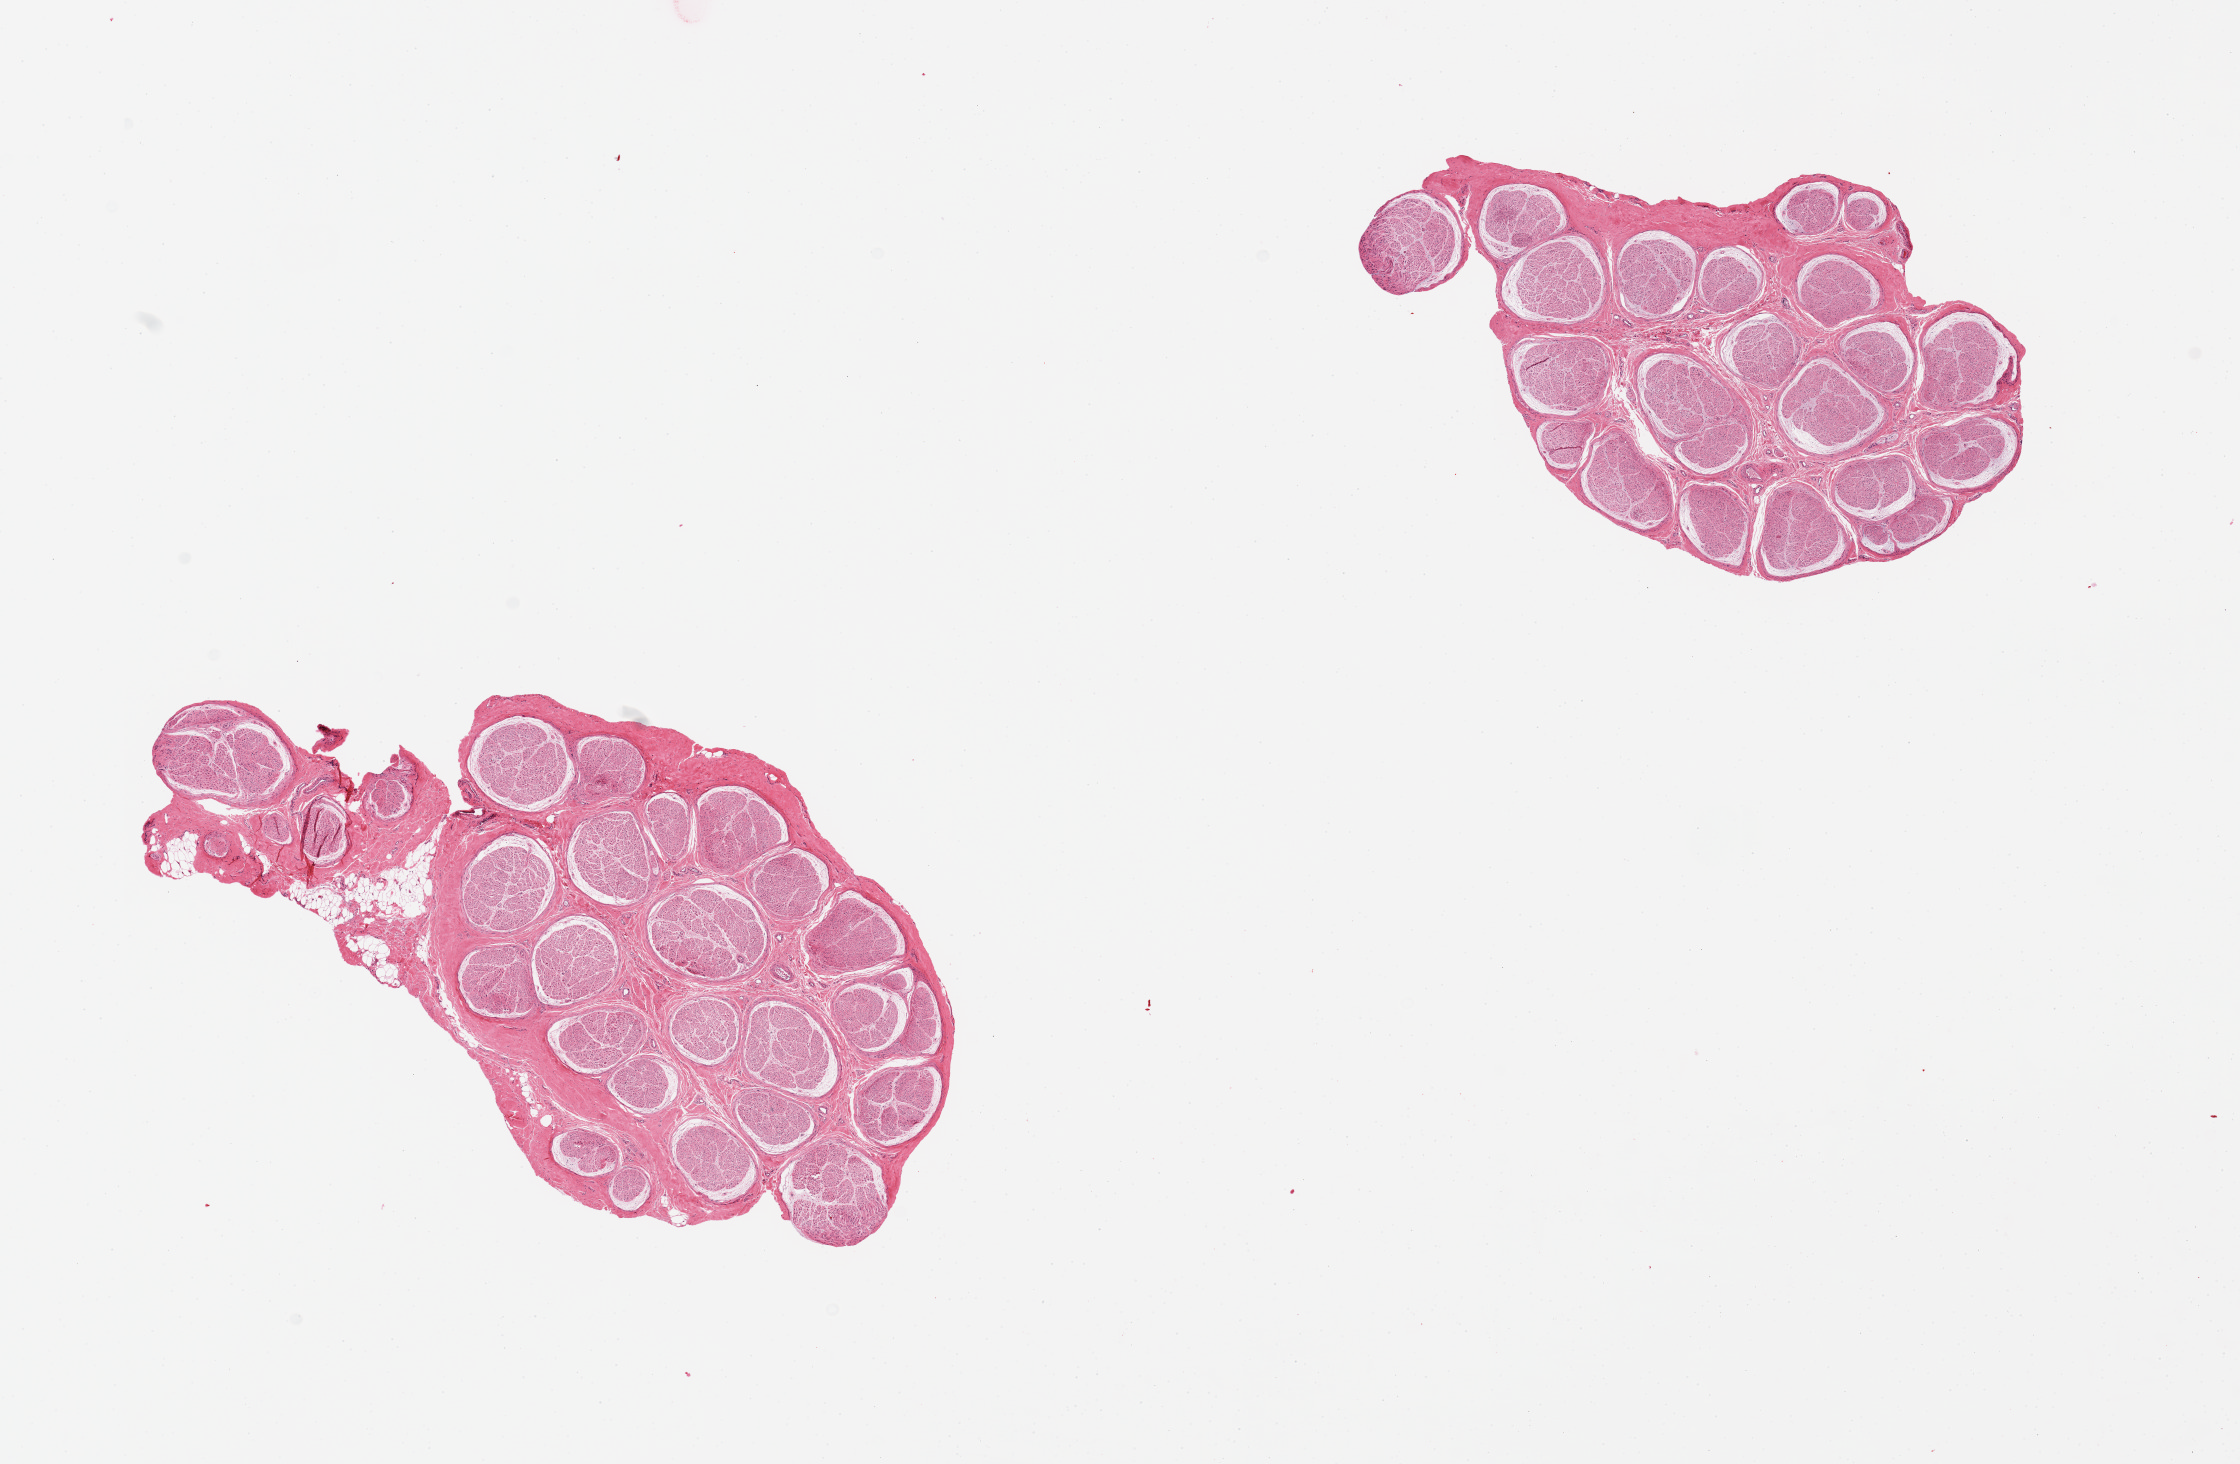
Whole-slide image, H&E stain, brightfield — whole scanned area (about 17.7 x 11.6 mm) shown as a low-resolution overview, PAXgene-fixed, paraffin-embedded tissue, section of tibial nerve (target tissue), tissue donor sample. Donor sex: male.
Review note (as recorded): 2 pieces, well trimmed.